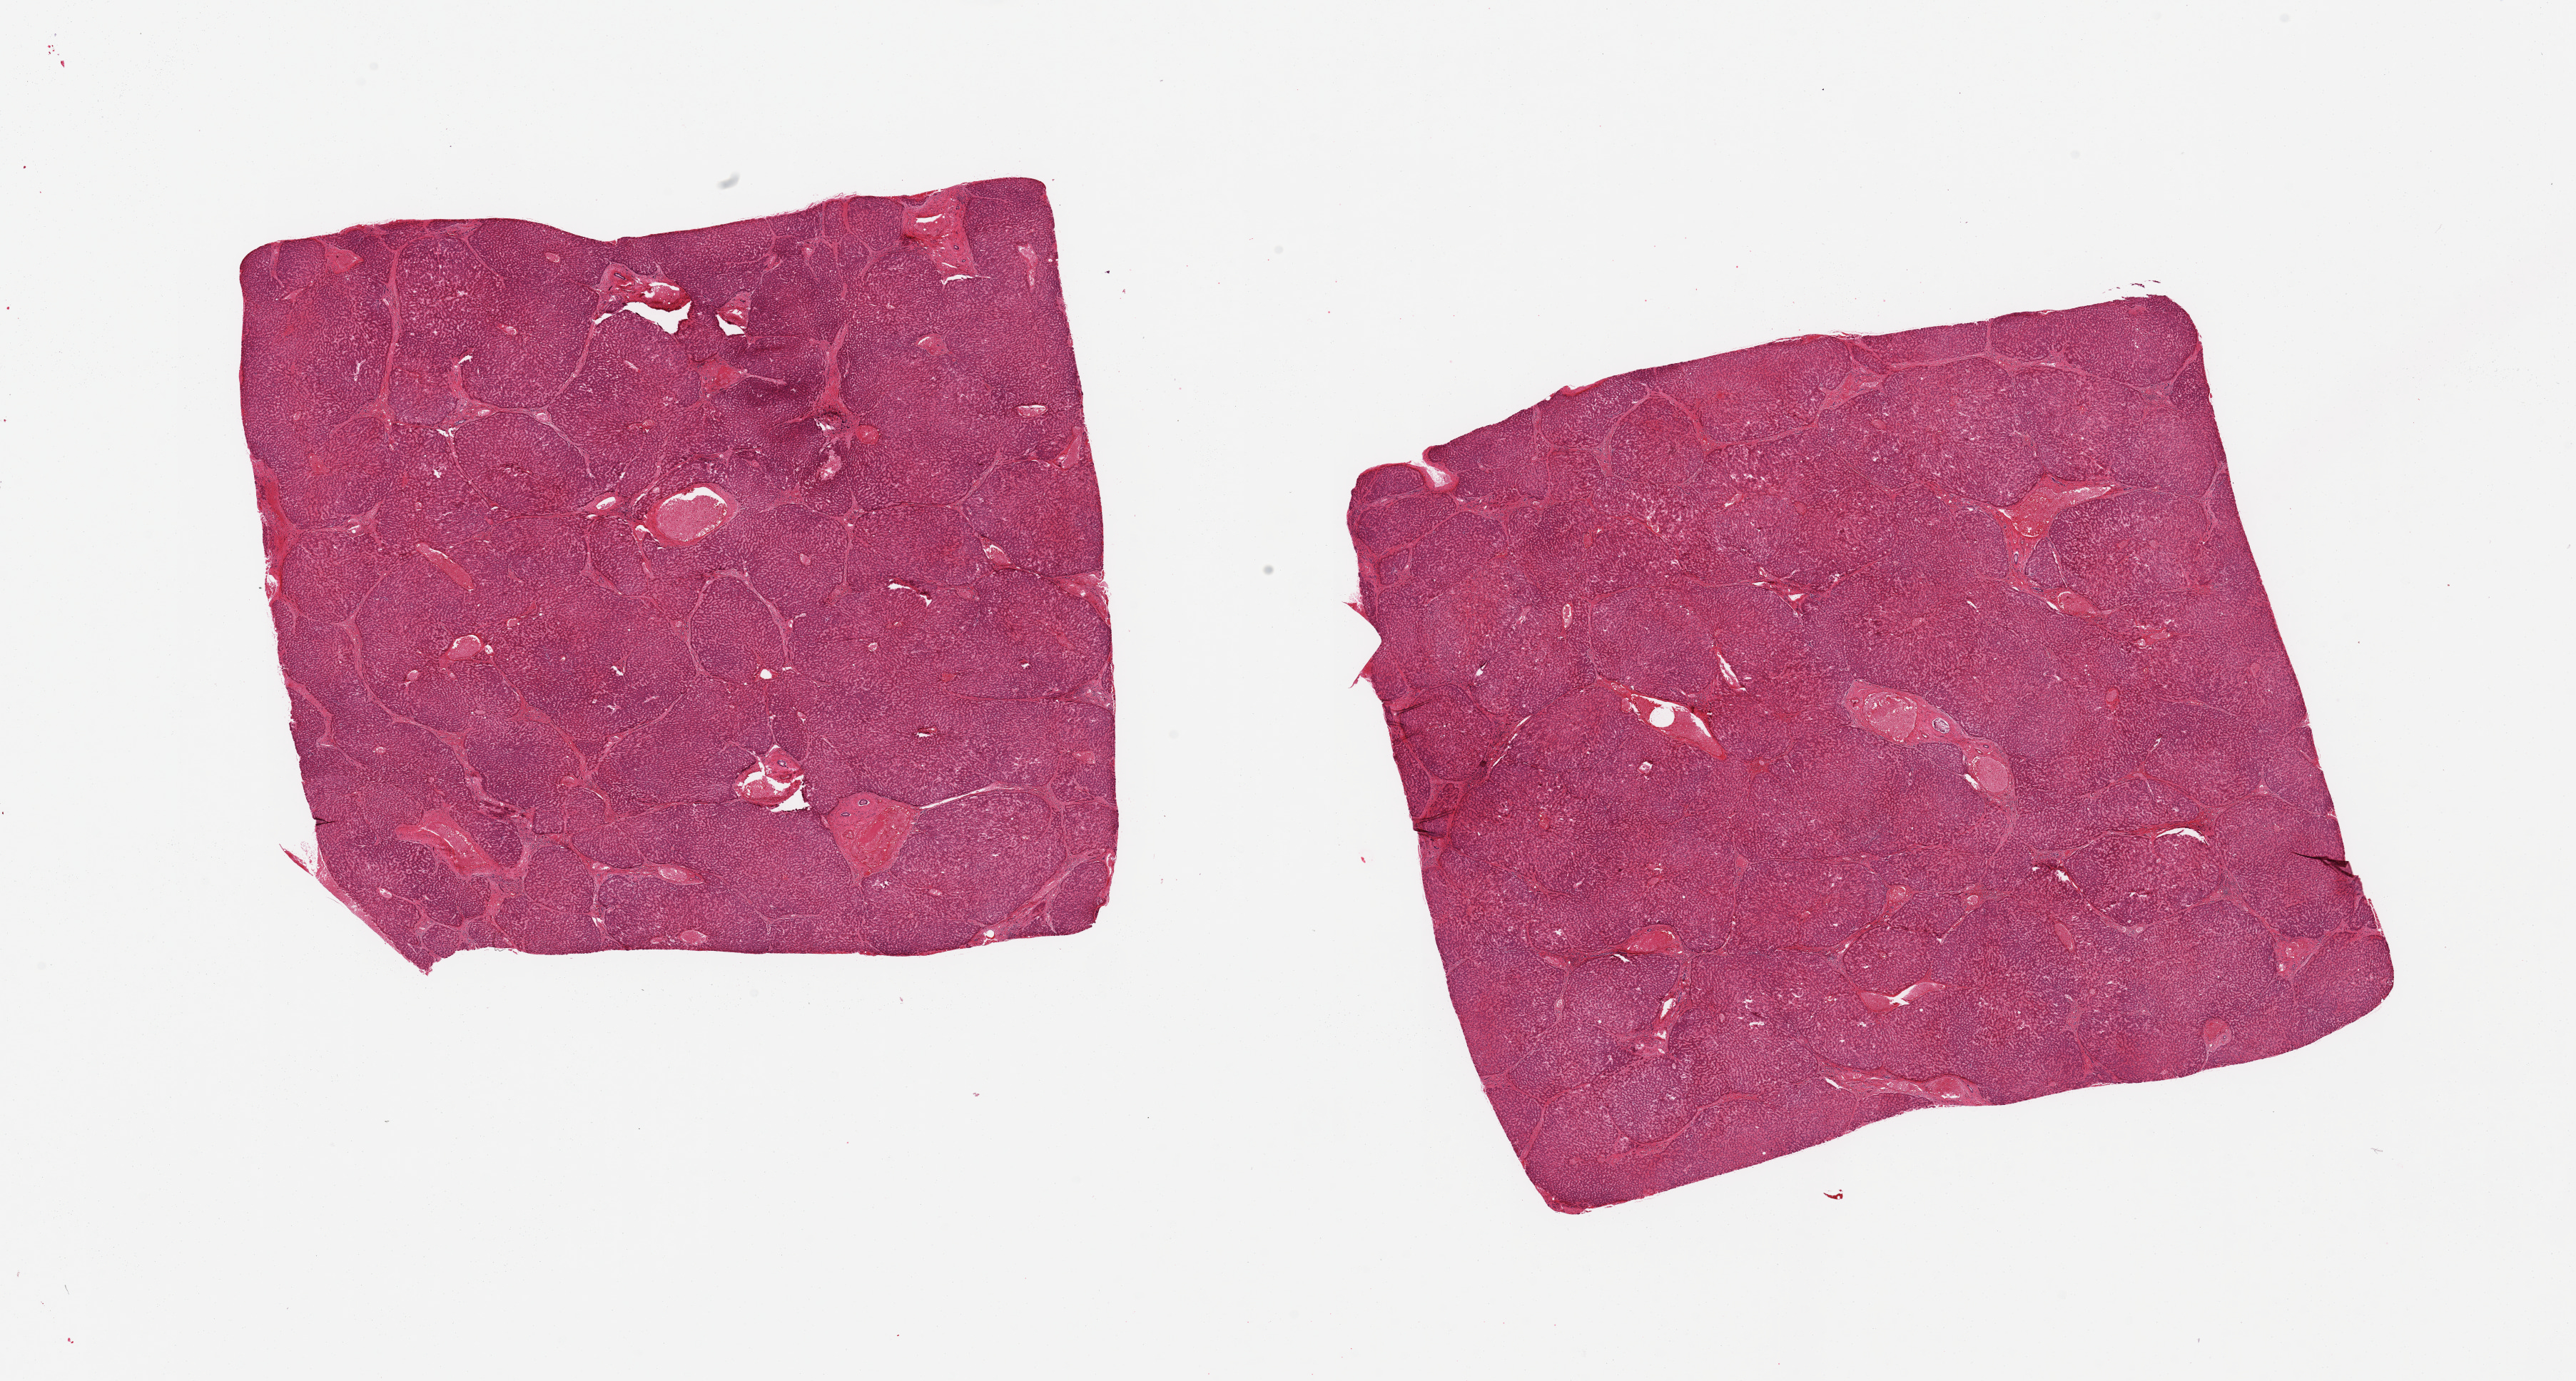
Whole-slide image, haematoxylin and eosin stain, brightfield — a low-resolution overview of the entire scanned area, about 28.5 x 15.3 mm (acquisition: 20x scan). PAXgene-fixed, paraffin-embedded tissue. Target tissue: liver. Tissue donor sample. Male donor.
Pathologist's review note for this sample: 2 pieces; congestion, bridging fibrosis/early cirrhosis, patchy mild chronic inflammation.